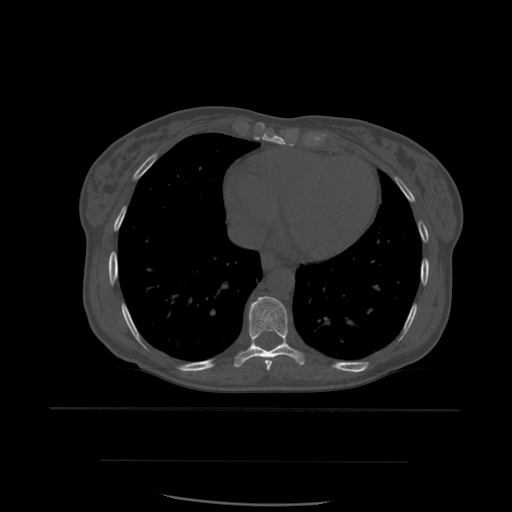
CT including the spine, one axial slice; position 338 of 574 along the scan axis; bone window (W 1800 / L 400 HU); 512 × 512 image matrix, field of view 392 × 392 mm. Patient age 48 years. Case-level facts recorded for this patient, not image findings: primary cancer: lung.
Annotated regions visible in this slice (semi-automatically segmented with operator editing):
- T8 vertebra: bounding box [x1, y1, x2, y2] px = [264, 360, 273, 371]
- T9 vertebra: [234, 297, 305, 368]